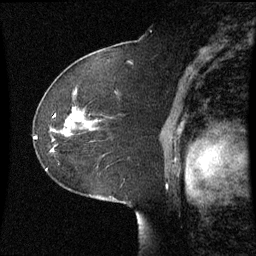
Breast MRI (dynamic contrast-enhanced), one sagittal slice; slice 42 of 60 in the series (ordered by position); dynamic contrast-enhanced series, image 2 of 3 at this slice position (ordered by acquisition); 1.5 T; TE 4.2 ms, TR 8.9 ms; 2.2 mm slice thickness; 256 × 256 image matrix, field of view 220 × 220 mm. Female patient, age 51 years. From the clinical record (not read from this slice): setting: breast cancer imaged before/during neoadjuvant chemotherapy; receptor status: HR-positive, HER2-negative.
Outlined on this slice (semi-automatically segmented with operator editing):
- analysis volume of interest (the breast-tissue region the enhancement analysis was run in; not a lesion): bounding box [x1, y1, x2, y2] px = [52, 108, 99, 153]
- tumour enhancement mask (voxels above the 70 % enhancement threshold inside the analysis volume of interest): [66, 112, 83, 127]